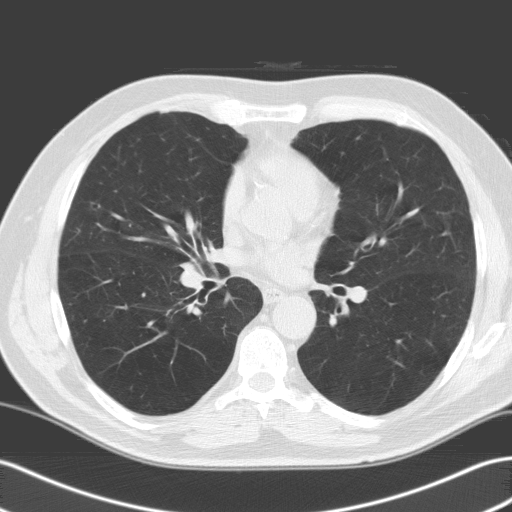
Axial slice from a low-dose chest CT screening exam, baseline annual screen, lung window (W 1500 / L -600 HU), standard (soft-tissue) reconstruction kernel (C). Male participant, aged 65 years at enrolment. Former smoker at enrolment.
Lesion marked by an expert reader, bounding box <68,189,115,230> (left, top, right, bottom; pixels). No non-calcified nodule or mass ≥4 mm was recorded by the screening reader at this exam. Participant outcome: lung cancer diagnosed 728 days after this screen — adenocarcinoma, NOS, right middle lobe, moderately differentiated (G2), stage IA (AJCC 6th edition), 25 mm at pathology.